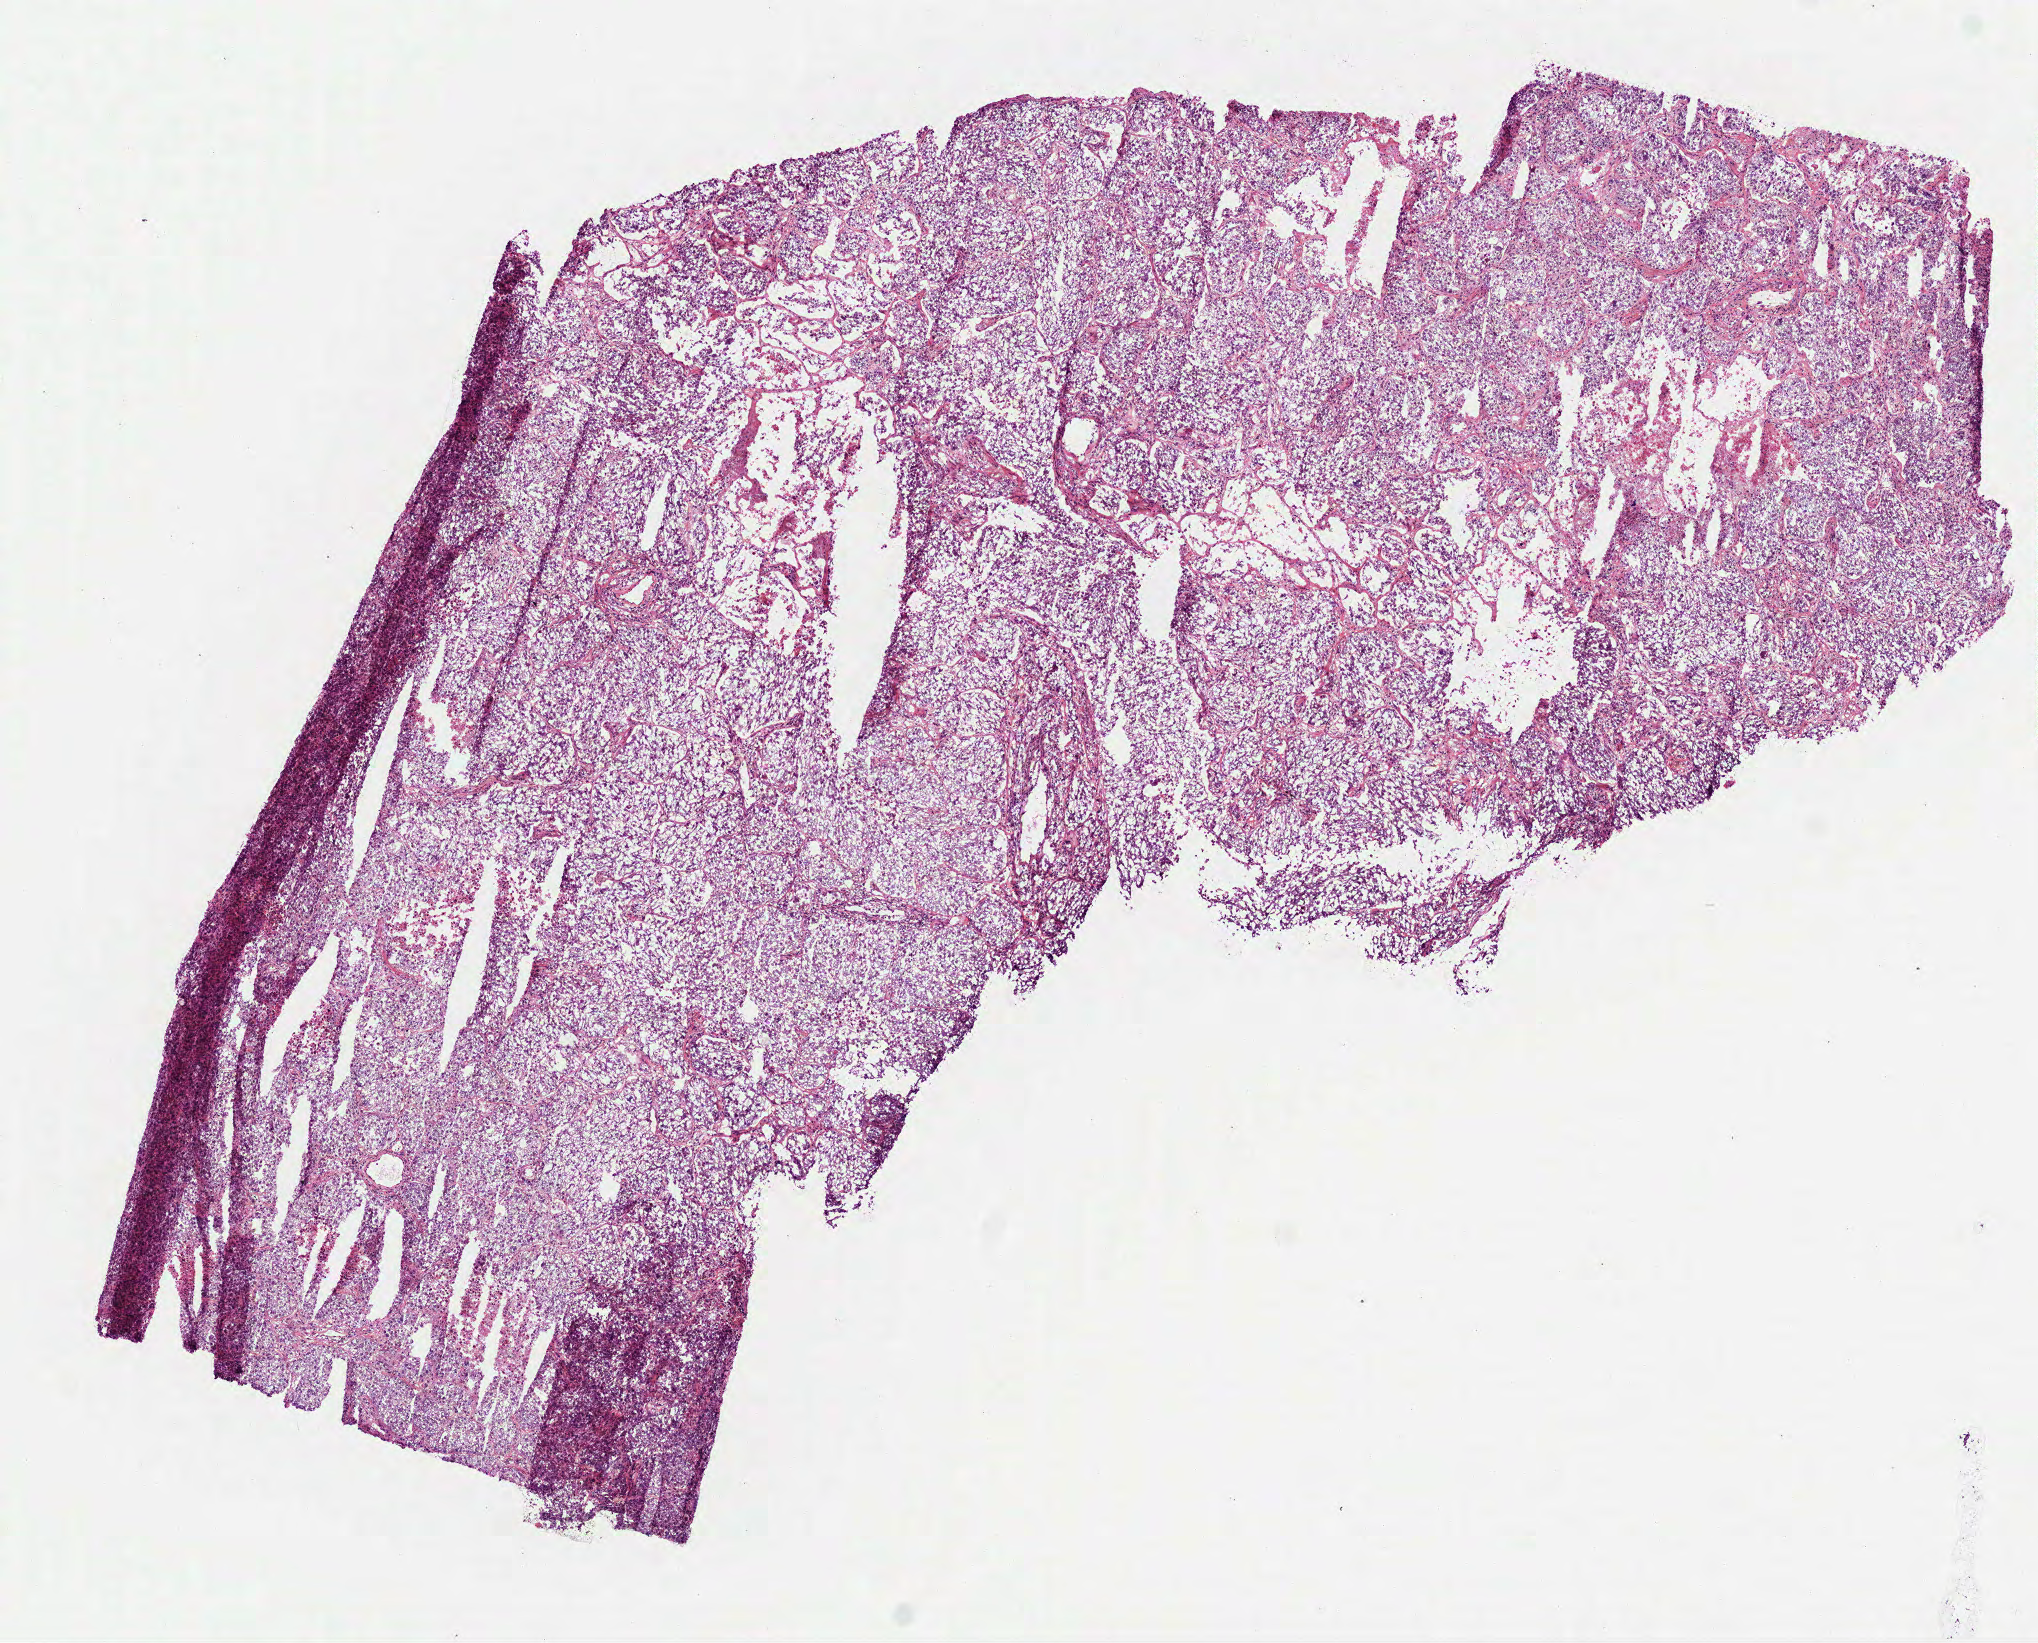
Whole-slide histology image, H&E — shown as a low-resolution overview of the whole scanned area (about 8.2 x 6.6 mm, slide scanned at 40x), frozen section, sample: primary tumour, lung. Patient: female, age at initial diagnosis 71 years. Slide review estimates, as recorded: tumour cells 77%, tumour nuclei 80%.
Diagnosis: Adenocarcinoma with mixed subtypes (lower lobe, lung).